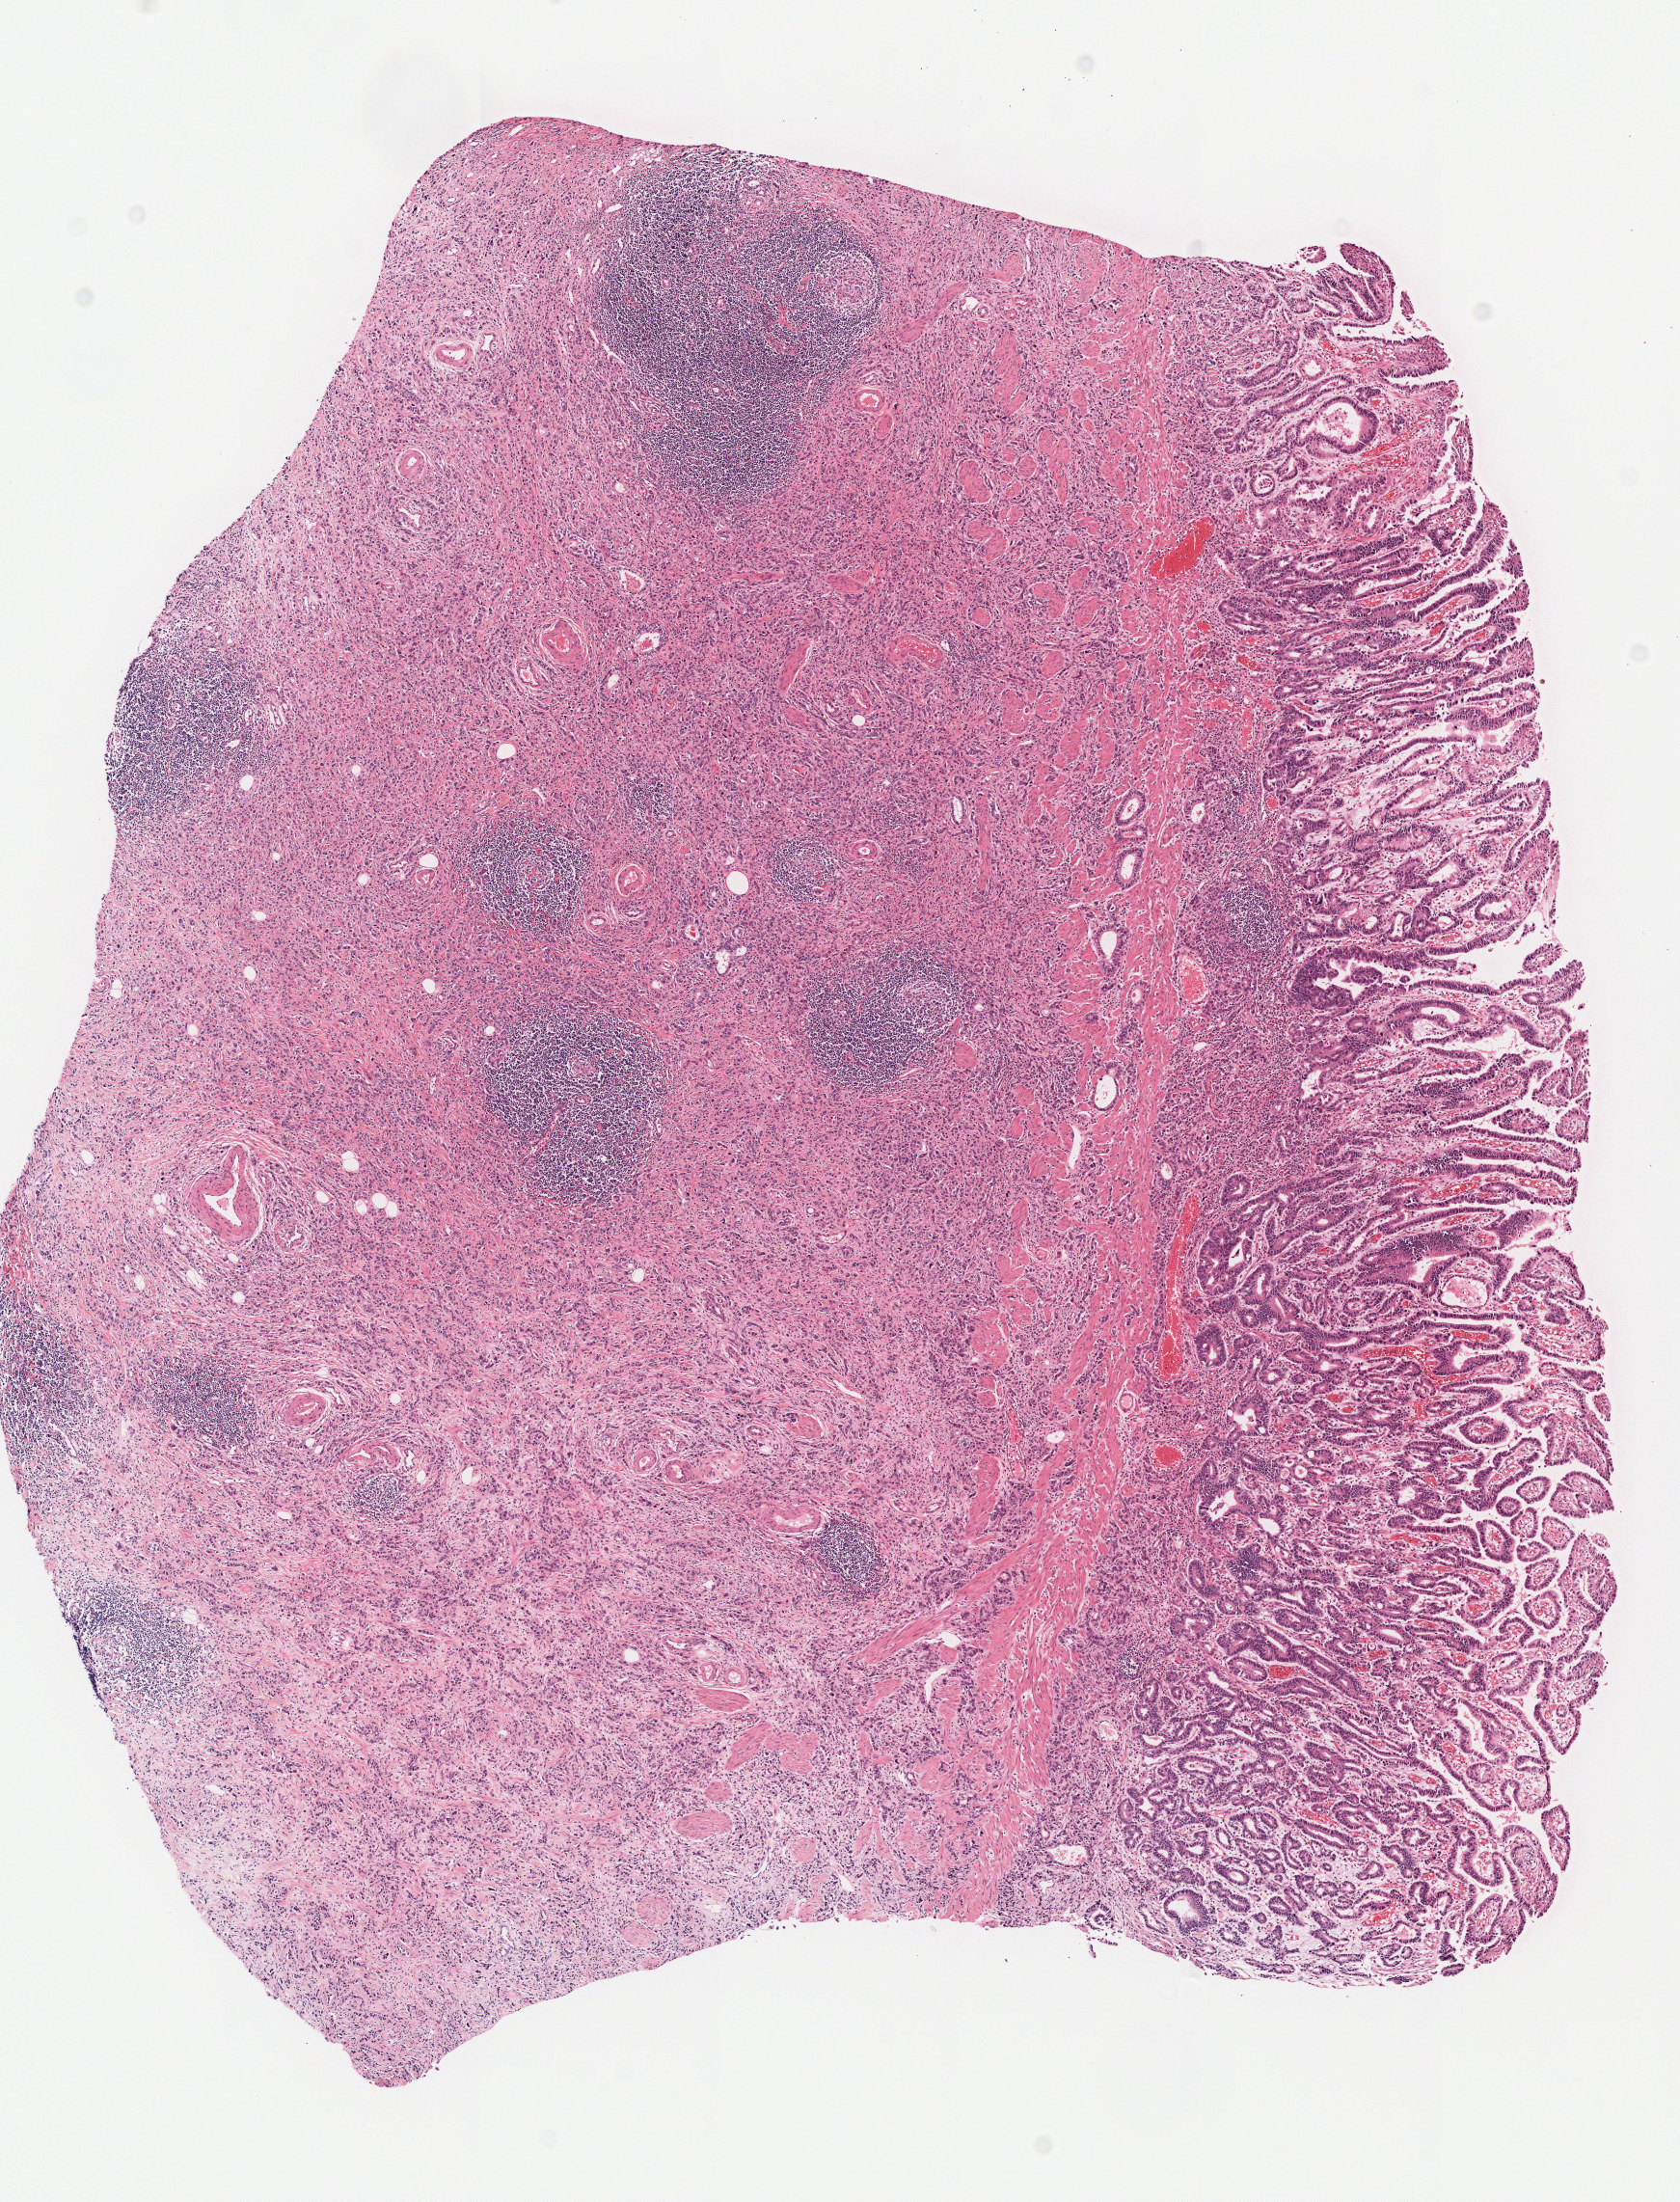
Hematoxylin and eosin (H&E) stained whole-slide image — shown as a low-resolution overview of the whole scanned area (about 6.9 x 9.0 mm). Formalin-fixed paraffin-embedded (FFPE) diagnostic section. Stomach, primary tumour sample. Female, age 62 years at initial diagnosis. Histologic grade: G2 (moderately differentiated).
Lymph nodes positive (case pathology): 2 of 63 examined. Pathologic diagnosis: Carcinoma, diffuse type. AJCC pathologic stage: IIA (7th edition).